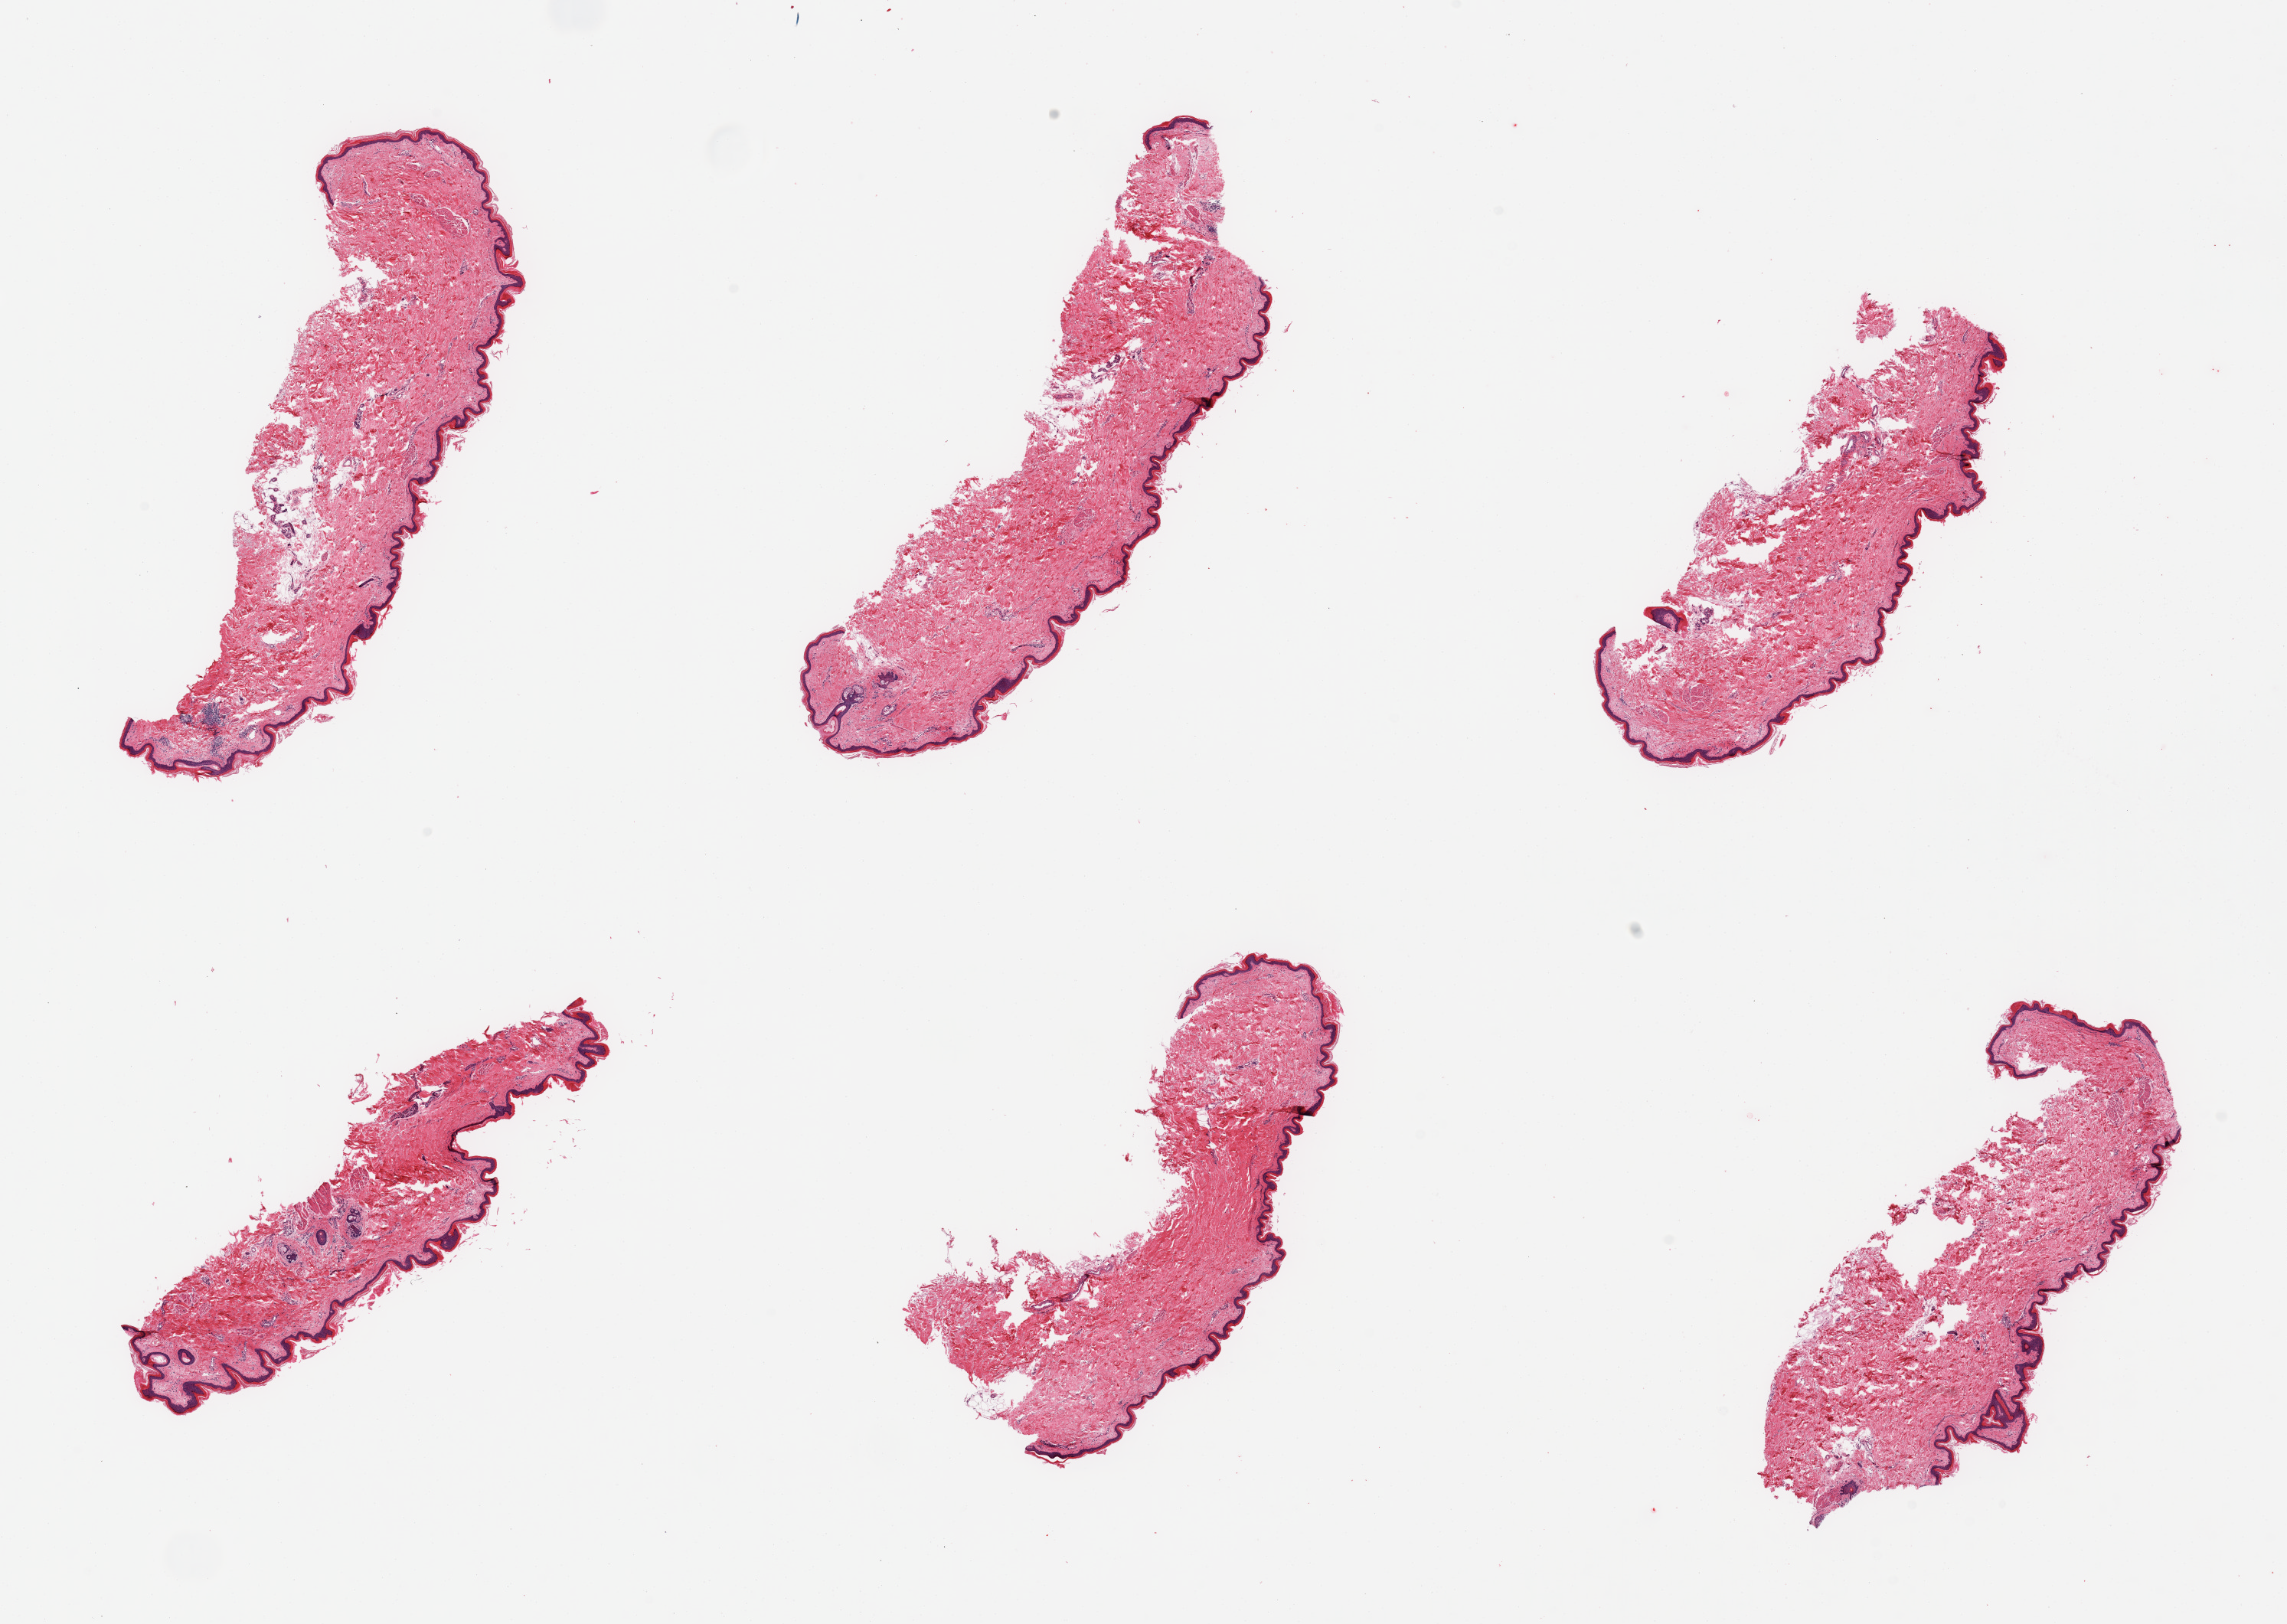
Digitized hematoxylin and eosin (H&E)-stained section, brightfield — low-resolution overview of the scanned area, about 23.6 x 16.8 mm; PAXgene-fixed paraffin-embedded (PFPE) section; target tissue: skin of lower leg; donor tissue sample. Donor sex: male.
* pathologist's review note for this sample: 6 pieces, no dermal fat; squamous epithelium is ~30-40 microns